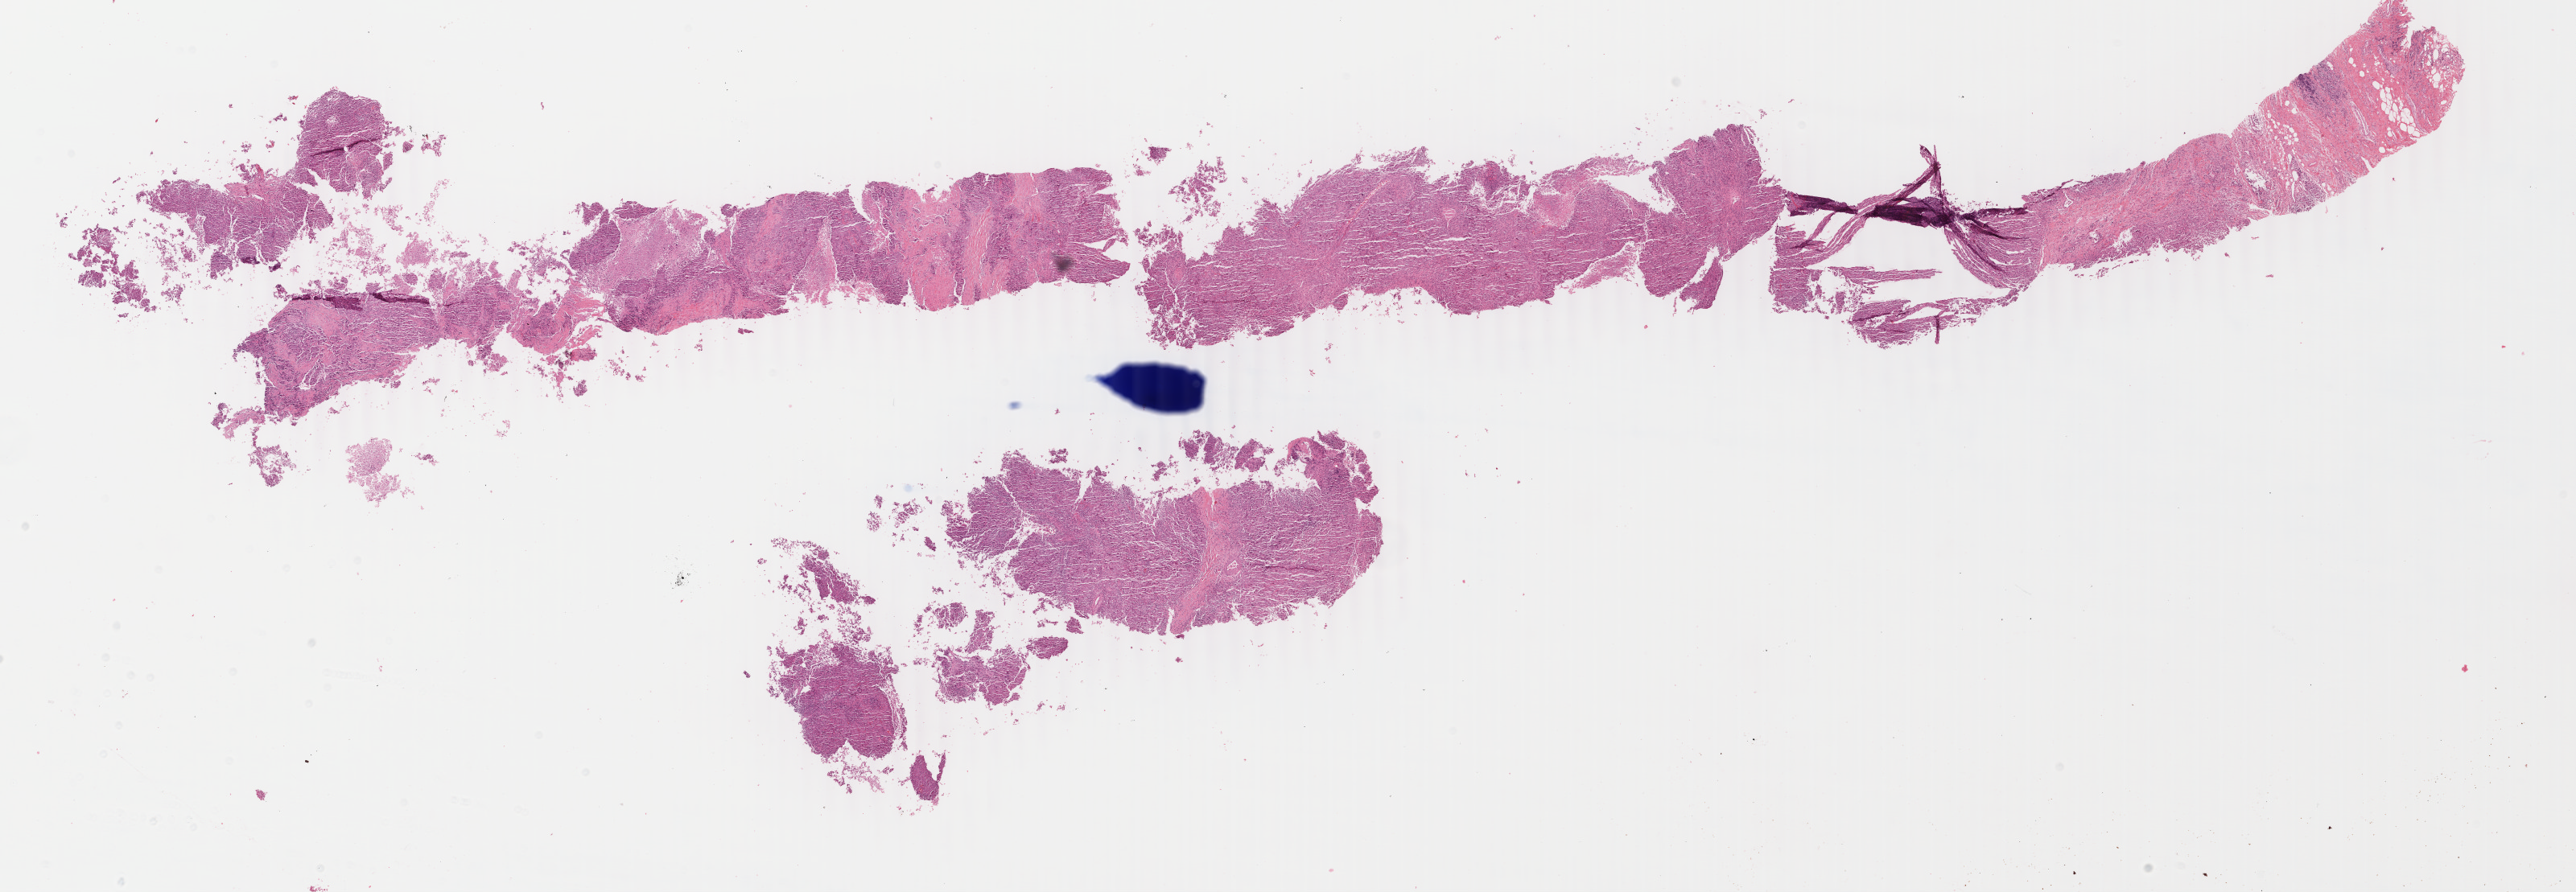
H&E-stained whole-slide image, whole scanned area (about 25.5 x 8.8 mm, acquisition: 40x scan) shown as a low-resolution overview; FFPE section; primary tumour sample from the breast. Patient: female, age at initial diagnosis 42 years.
* diagnosis: Infiltrating duct carcinoma, NOS
* AJCC pathologic stage: IIB
* lymph nodes positive (case pathology): 0 of 27 examined
* laterality: right